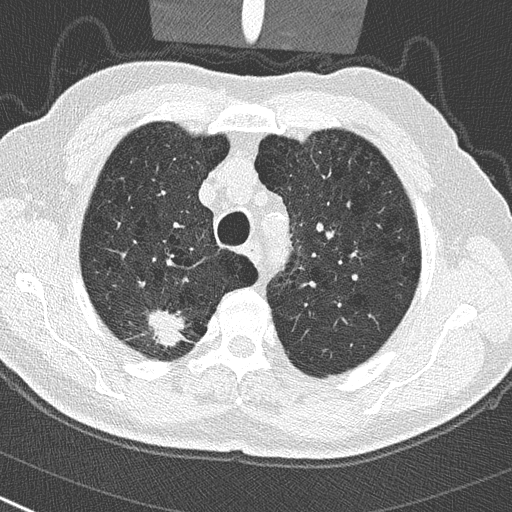
Low-dose screening chest CT, one axial slice; slice 229 of 290 in the series (ordered by position); reconstruction kernel B50f; 120 kVp; lung window (W 1500 / L -600 HU); 2 mm slice thickness; 512 × 512 image matrix, field of view 300 × 300 mm.
Outlined on this slice (manually delineated by an expert):
- lesion 1 (tumor, upper lobe of right lung): bounding box (x1, y1, x2, y2) in pixels: (146, 309, 186, 351)